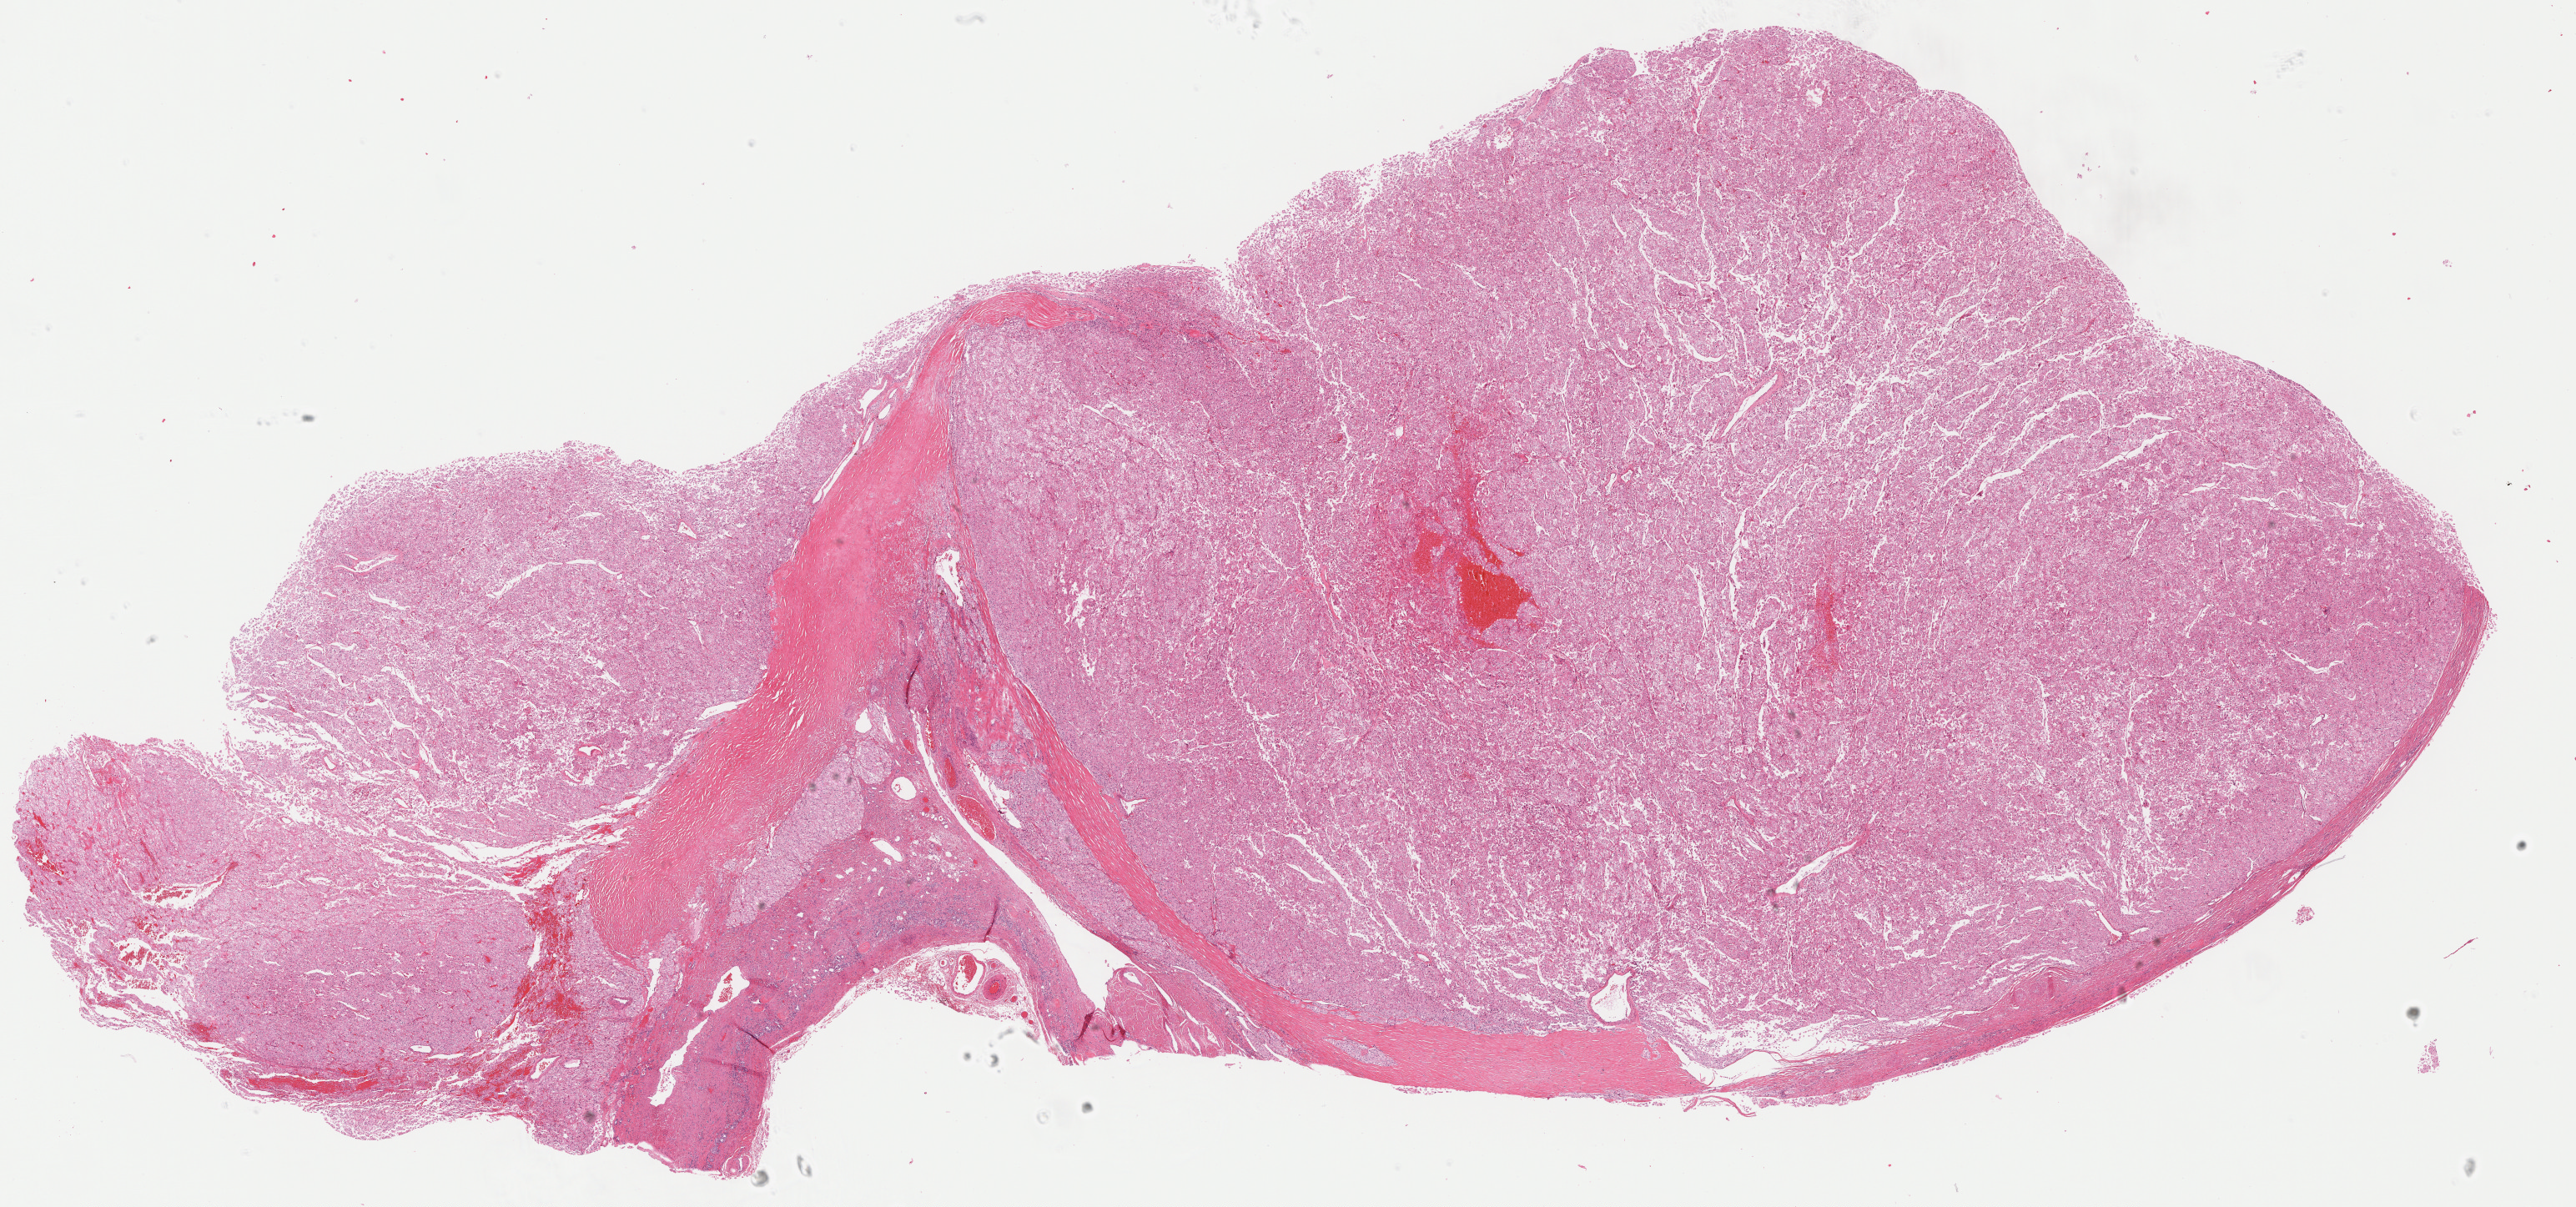
Digitized Hematoxylin and eosin (H&E) stained tissue section (whole slide), whole scanned area (about 24.9 x 11.7 mm, acquisition: 40x scan) shown as a low-resolution overview, FFPE section, sample: primary tumour, kidney. Patient: female, age at initial diagnosis 35 years.
Pathologic diagnosis: Renal cell carcinoma, chromophobe type.